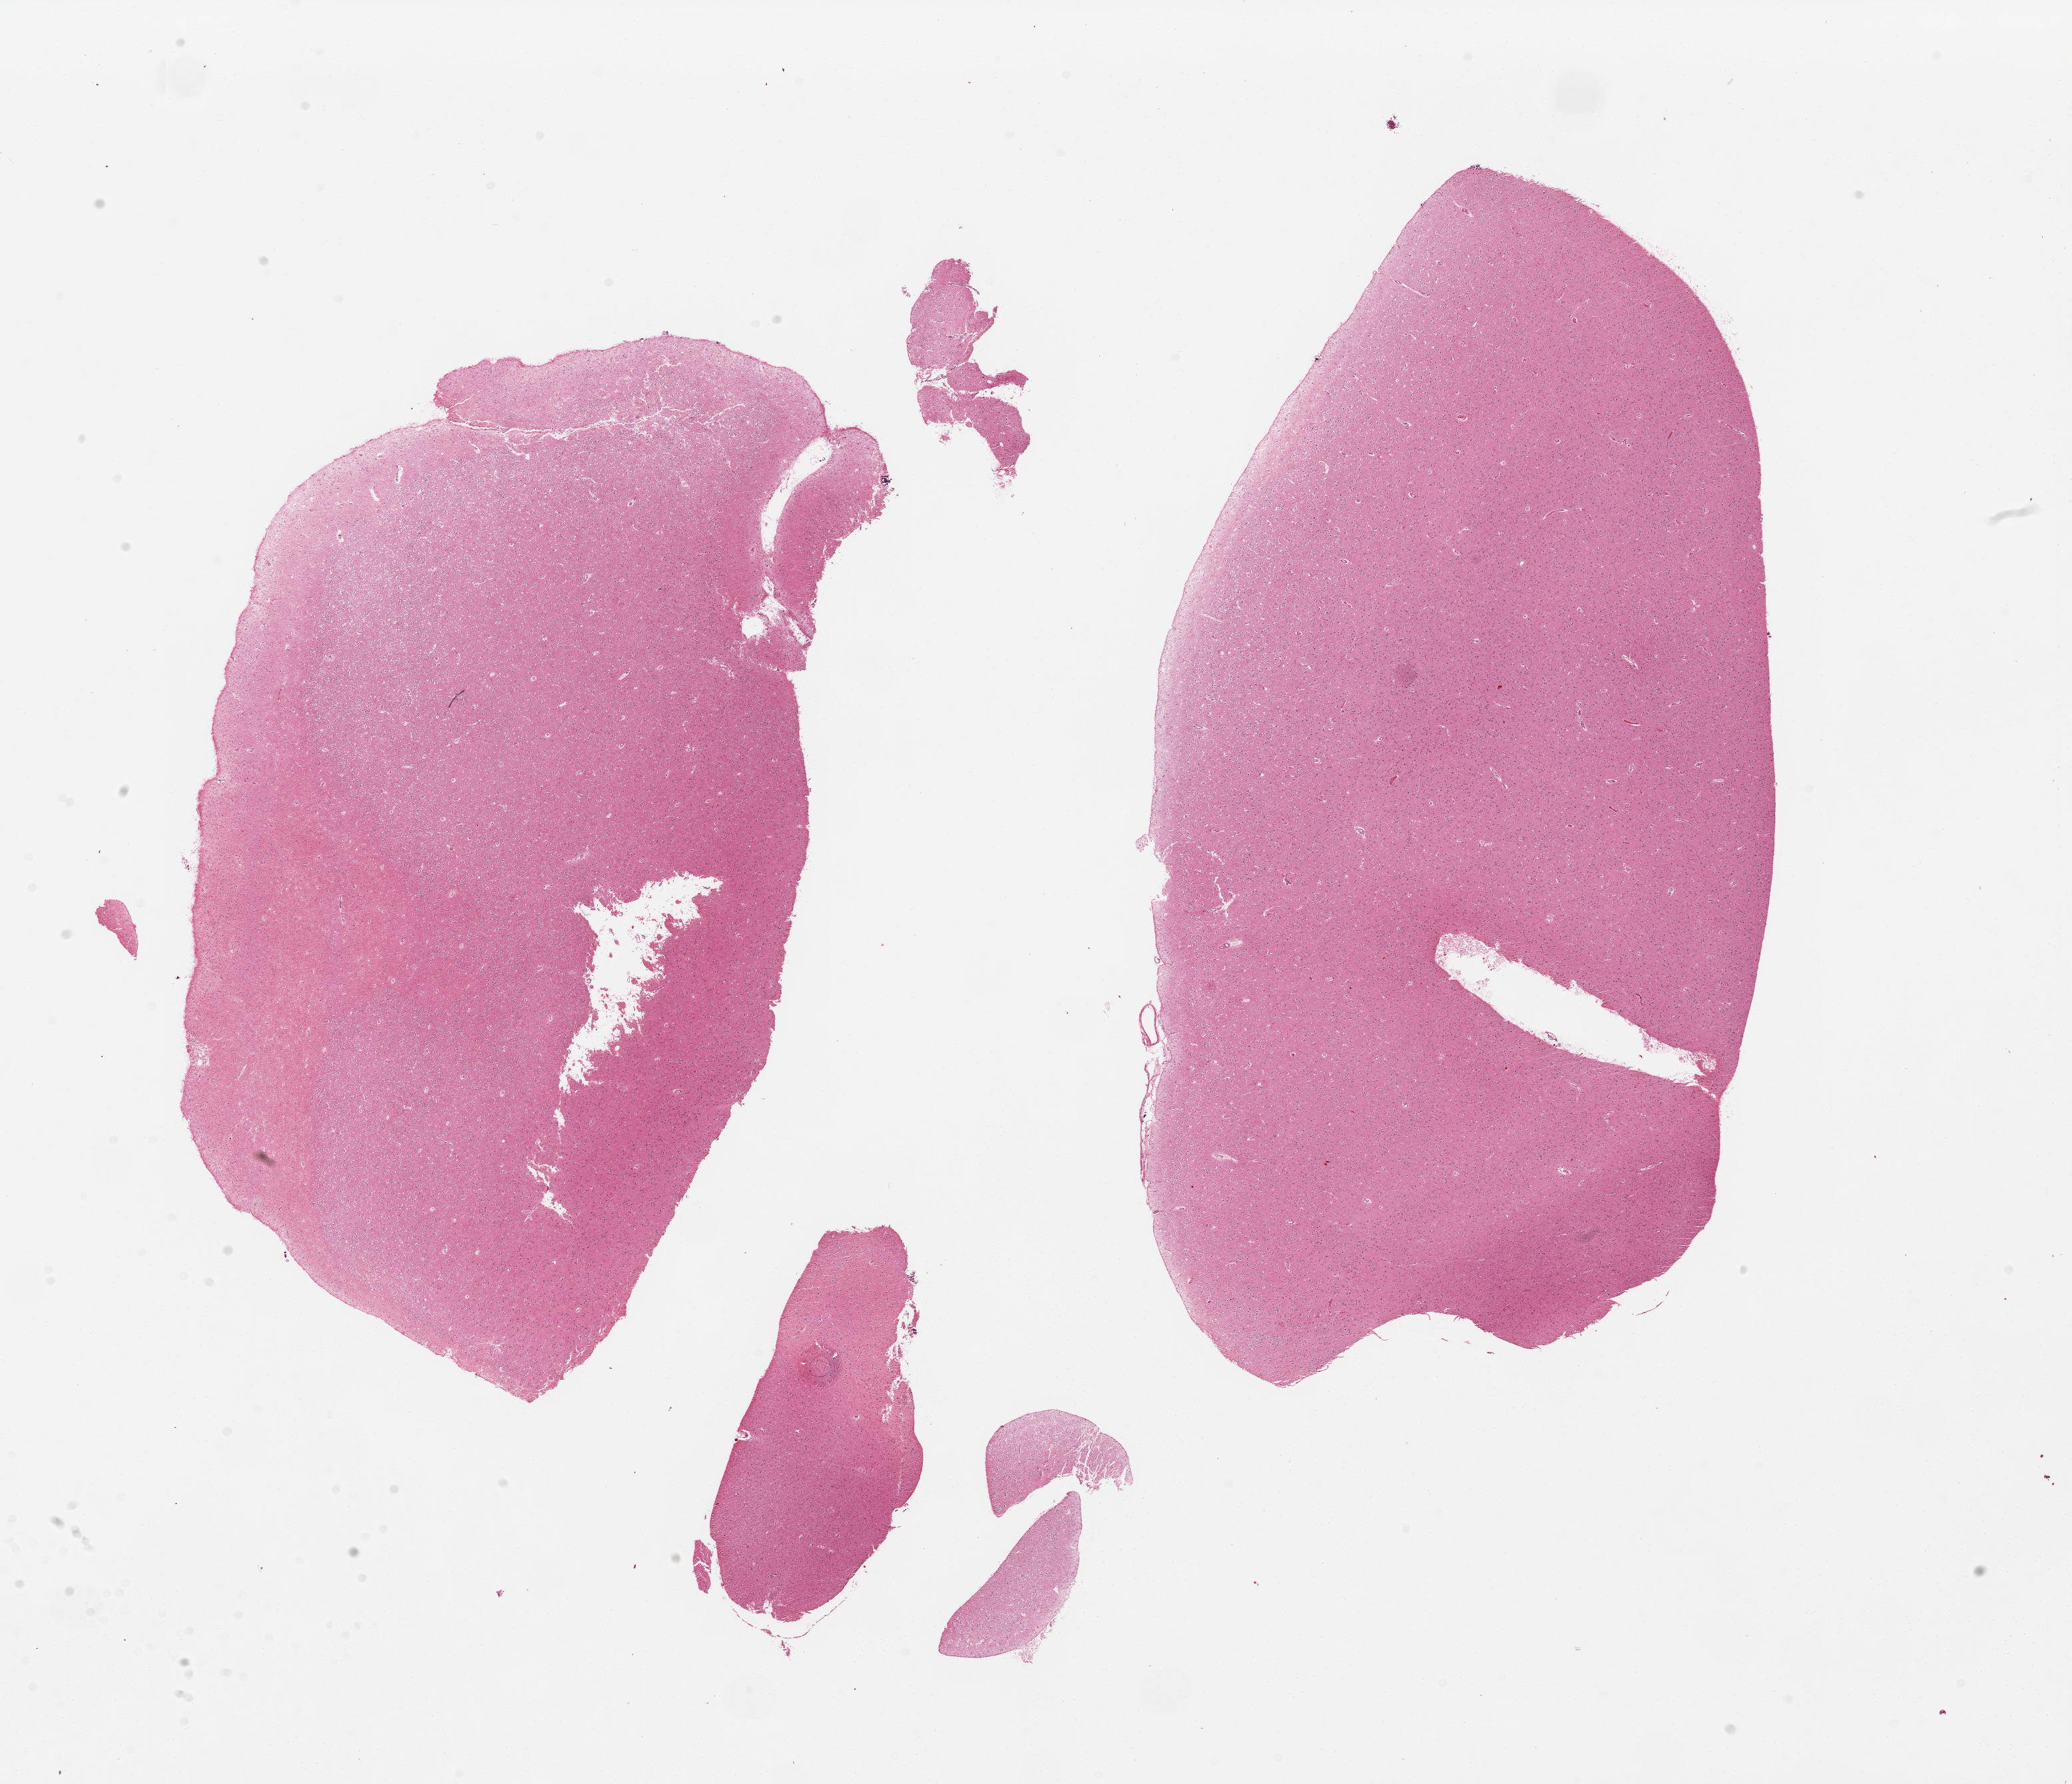
Whole-slide image, H&E stain, a low-resolution overview of the entire scanned area, about 24.6 x 21.2 mm; PAXgene-fixed paraffin-embedded (PFPE) section; section of cerebral cortex (target tissue); donor tissue sample. Donor: male.
* pathologist's review note for this sample: 2 pieces, no abnormalities